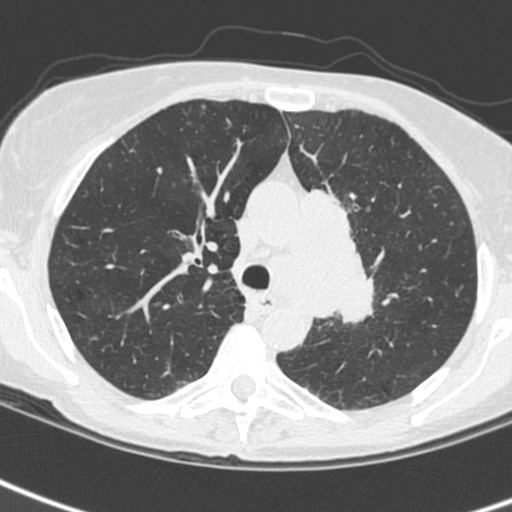
Low-dose screening chest CT, one axial slice. Slice 170 of 242 in the series (ordered by position). 120 kVp. Lung window (W 1500 / L -600 HU). 512 × 512 image matrix, field of view 284 × 284 mm.
Outlined on this slice (outlined manually by an expert reader):
- lesion 3 (tumor, upper lobe of left lung): bounding box [x1, y1, x2, y2] px = [307, 188, 374, 323]